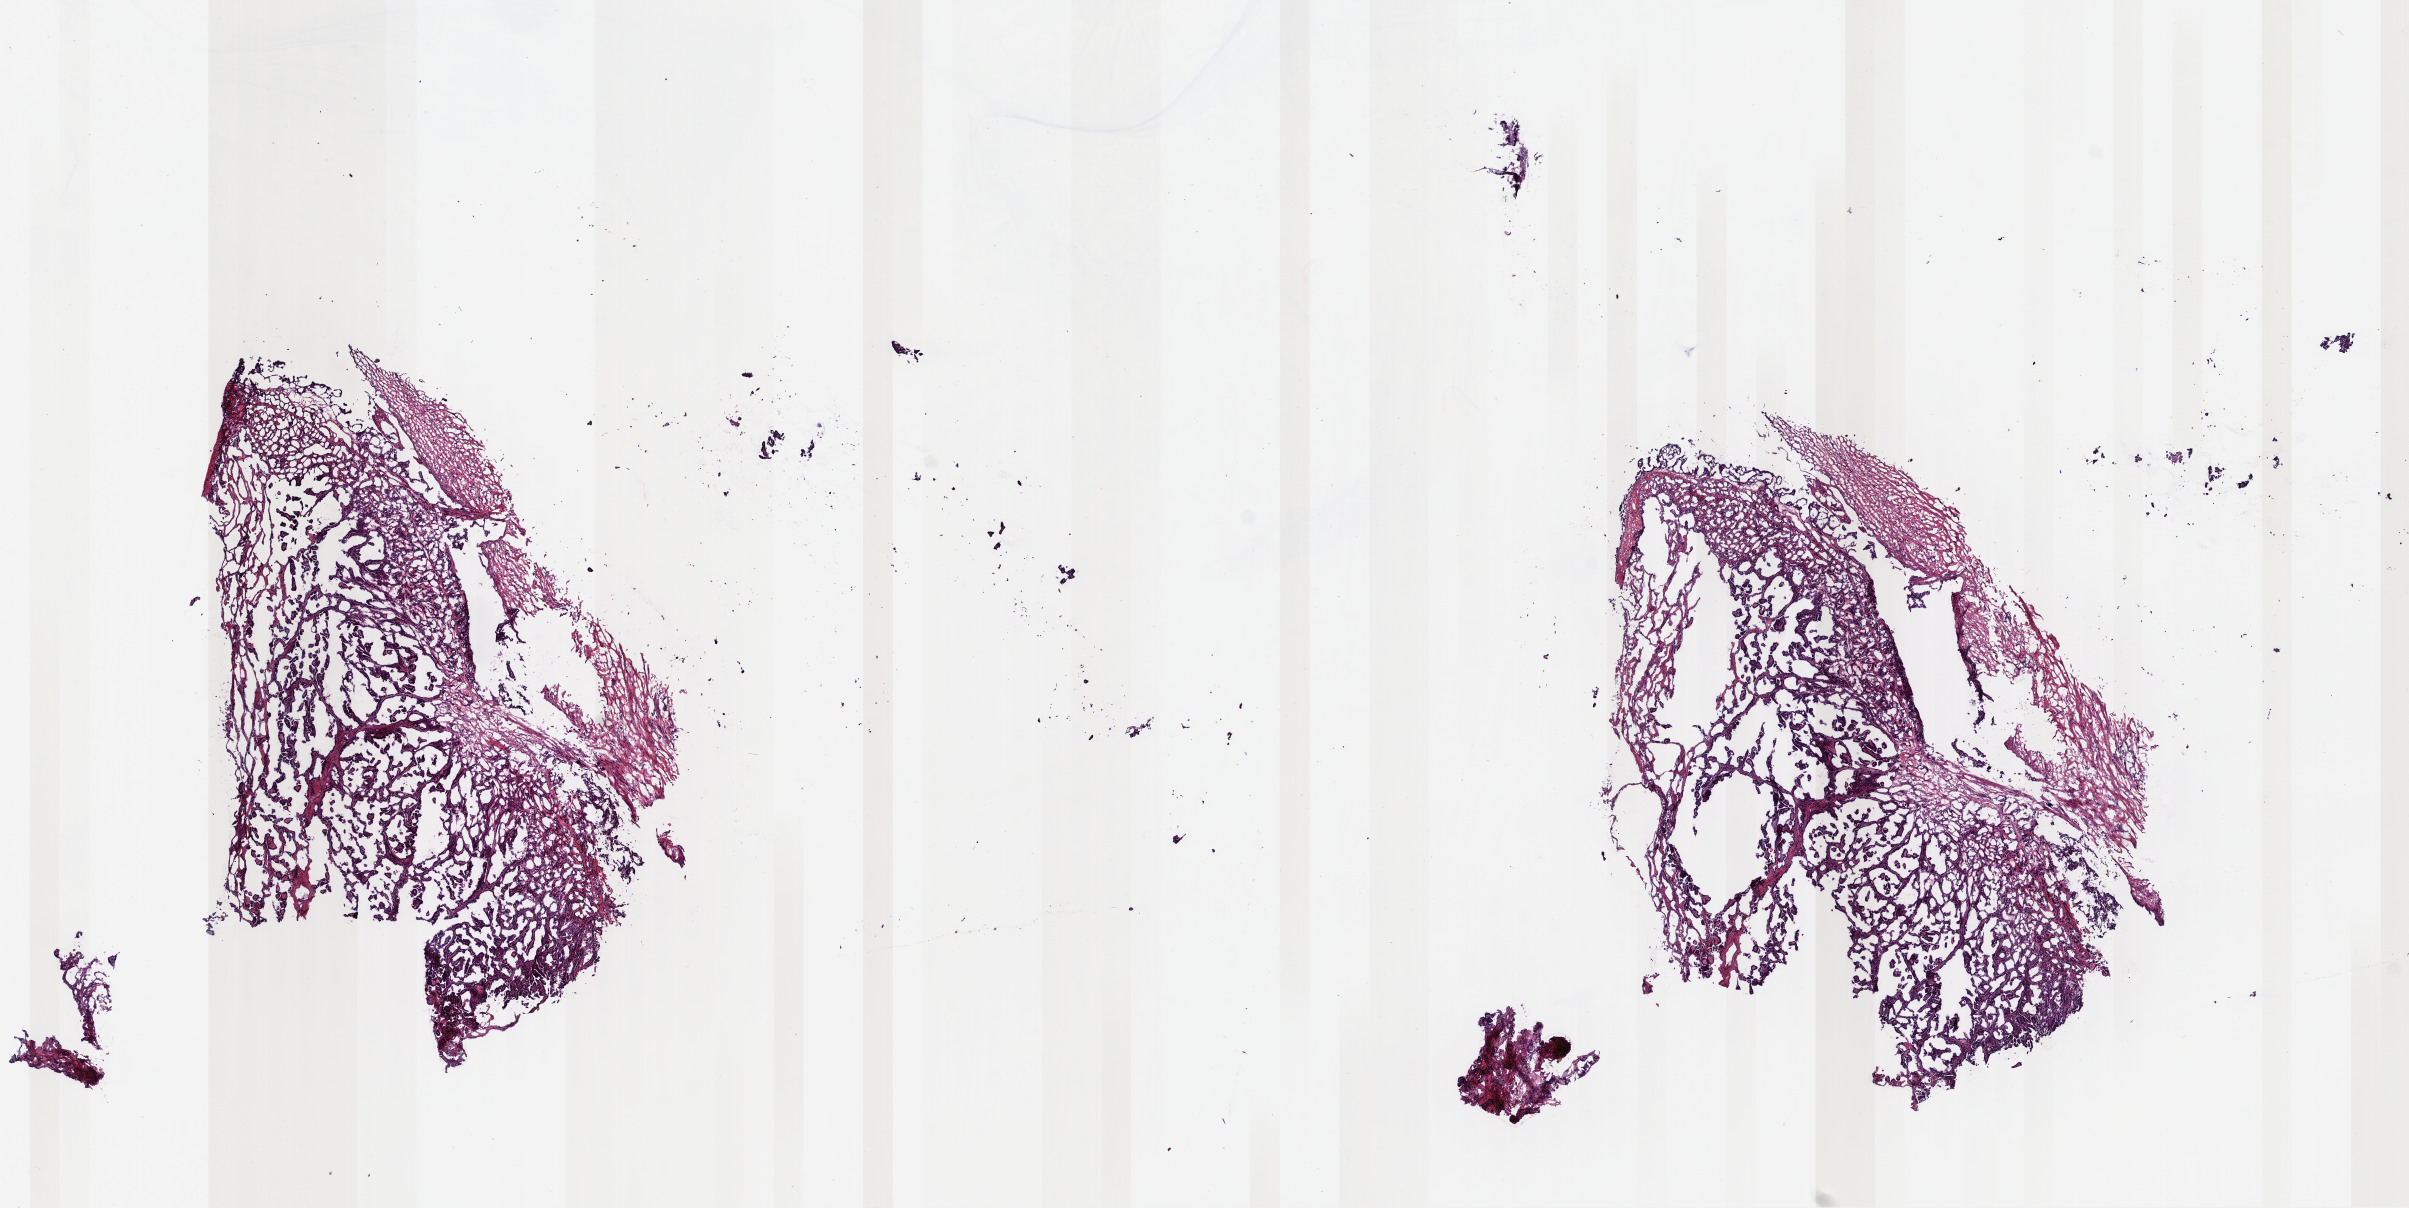
H&E-stained whole-slide image, low-resolution overview of the scanned area, about 18.9 x 9.5 mm. Frozen section from the top of the tissue portion. Sample: primary tumour, mesothelium. Female patient; age at initial diagnosis 66 years. Slide review estimates, as recorded: tumour cells 100%, tumour nuclei 85%, normal cells 0%, stromal cells 0%, necrosis 0%. Infiltration values recorded for this section: lymphocyte infiltration 0%, monocyte infiltration 0%, neutrophil infiltration 0%.
* TNM: T3 N1 M0
* AJCC pathologic stage: III (7th edition)
* histologic diagnosis: Mesothelioma, biphasic, malignant